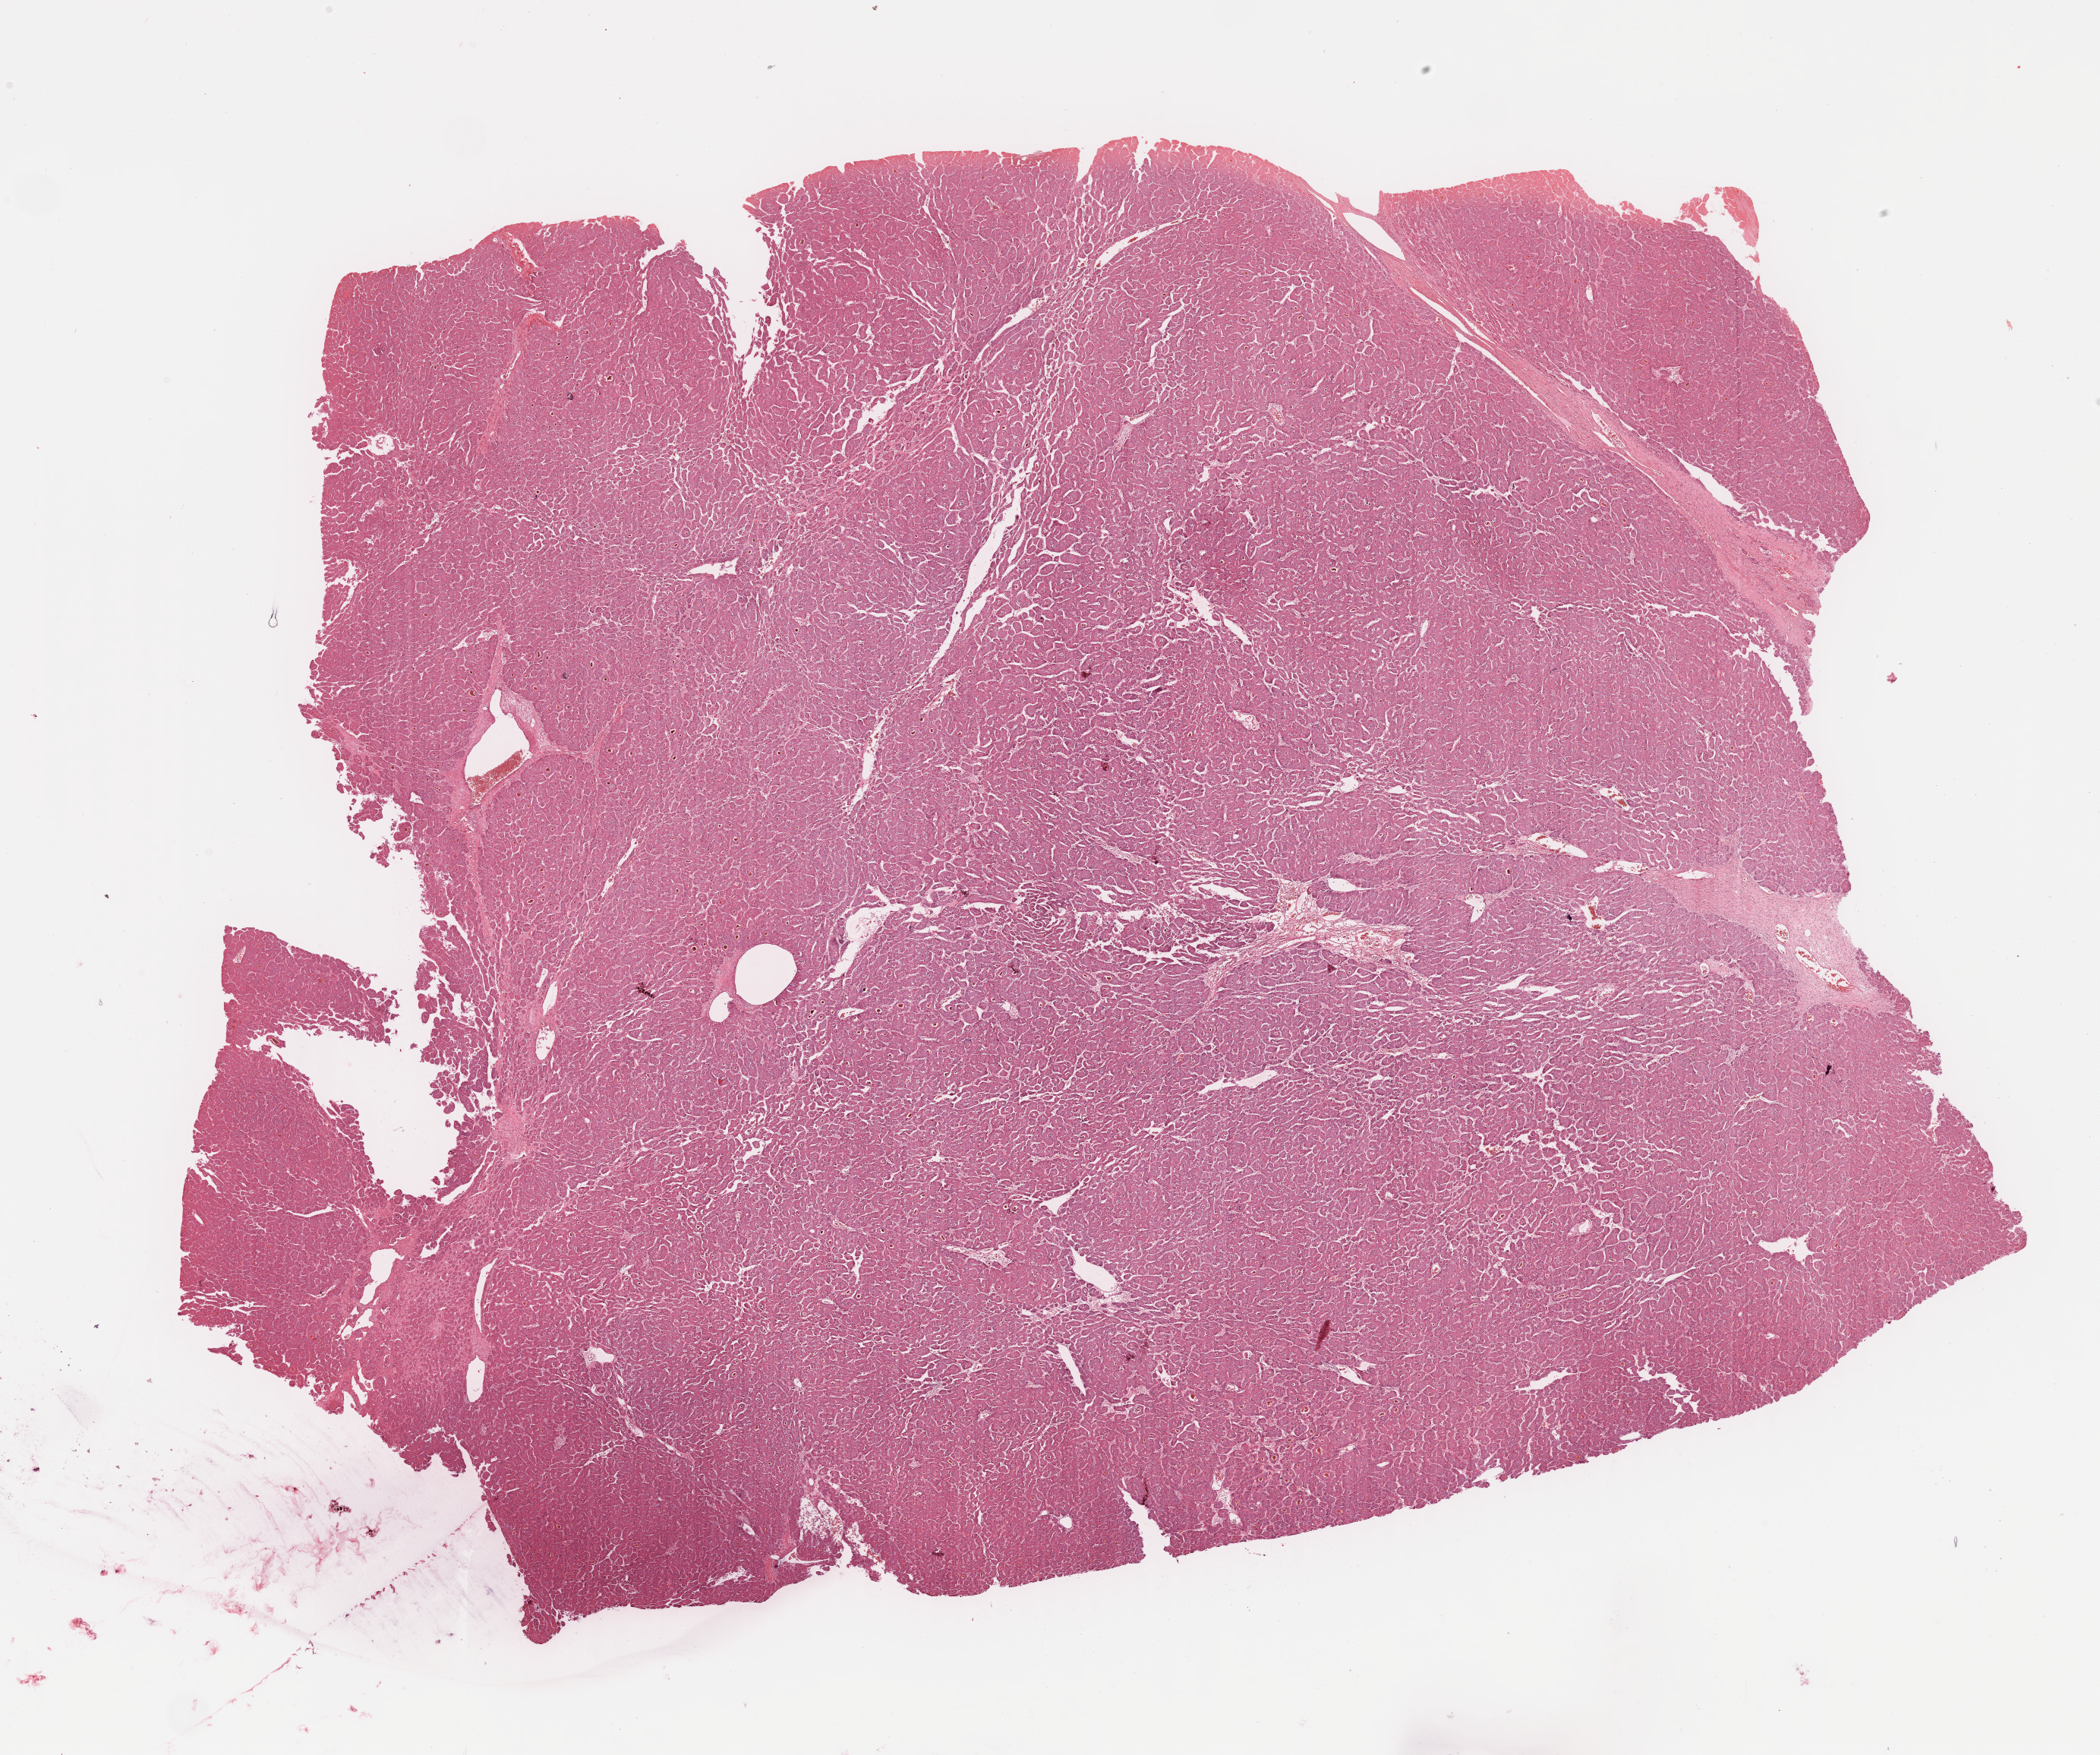
Digitized Hematoxylin and eosin (H&E) stained tissue section (whole slide) — shown as a low-resolution overview of the whole scanned area (about 22.4 x 18.7 mm, slide scanned at 40x), formalin-fixed paraffin-embedded (FFPE) diagnostic section, sample: primary tumour, liver. Male patient; age at initial diagnosis 45 years. Histologic grade: G2 (moderately differentiated).
- diagnosis: Hepatocellular carcinoma, NOS
- AJCC pathologic stage: I